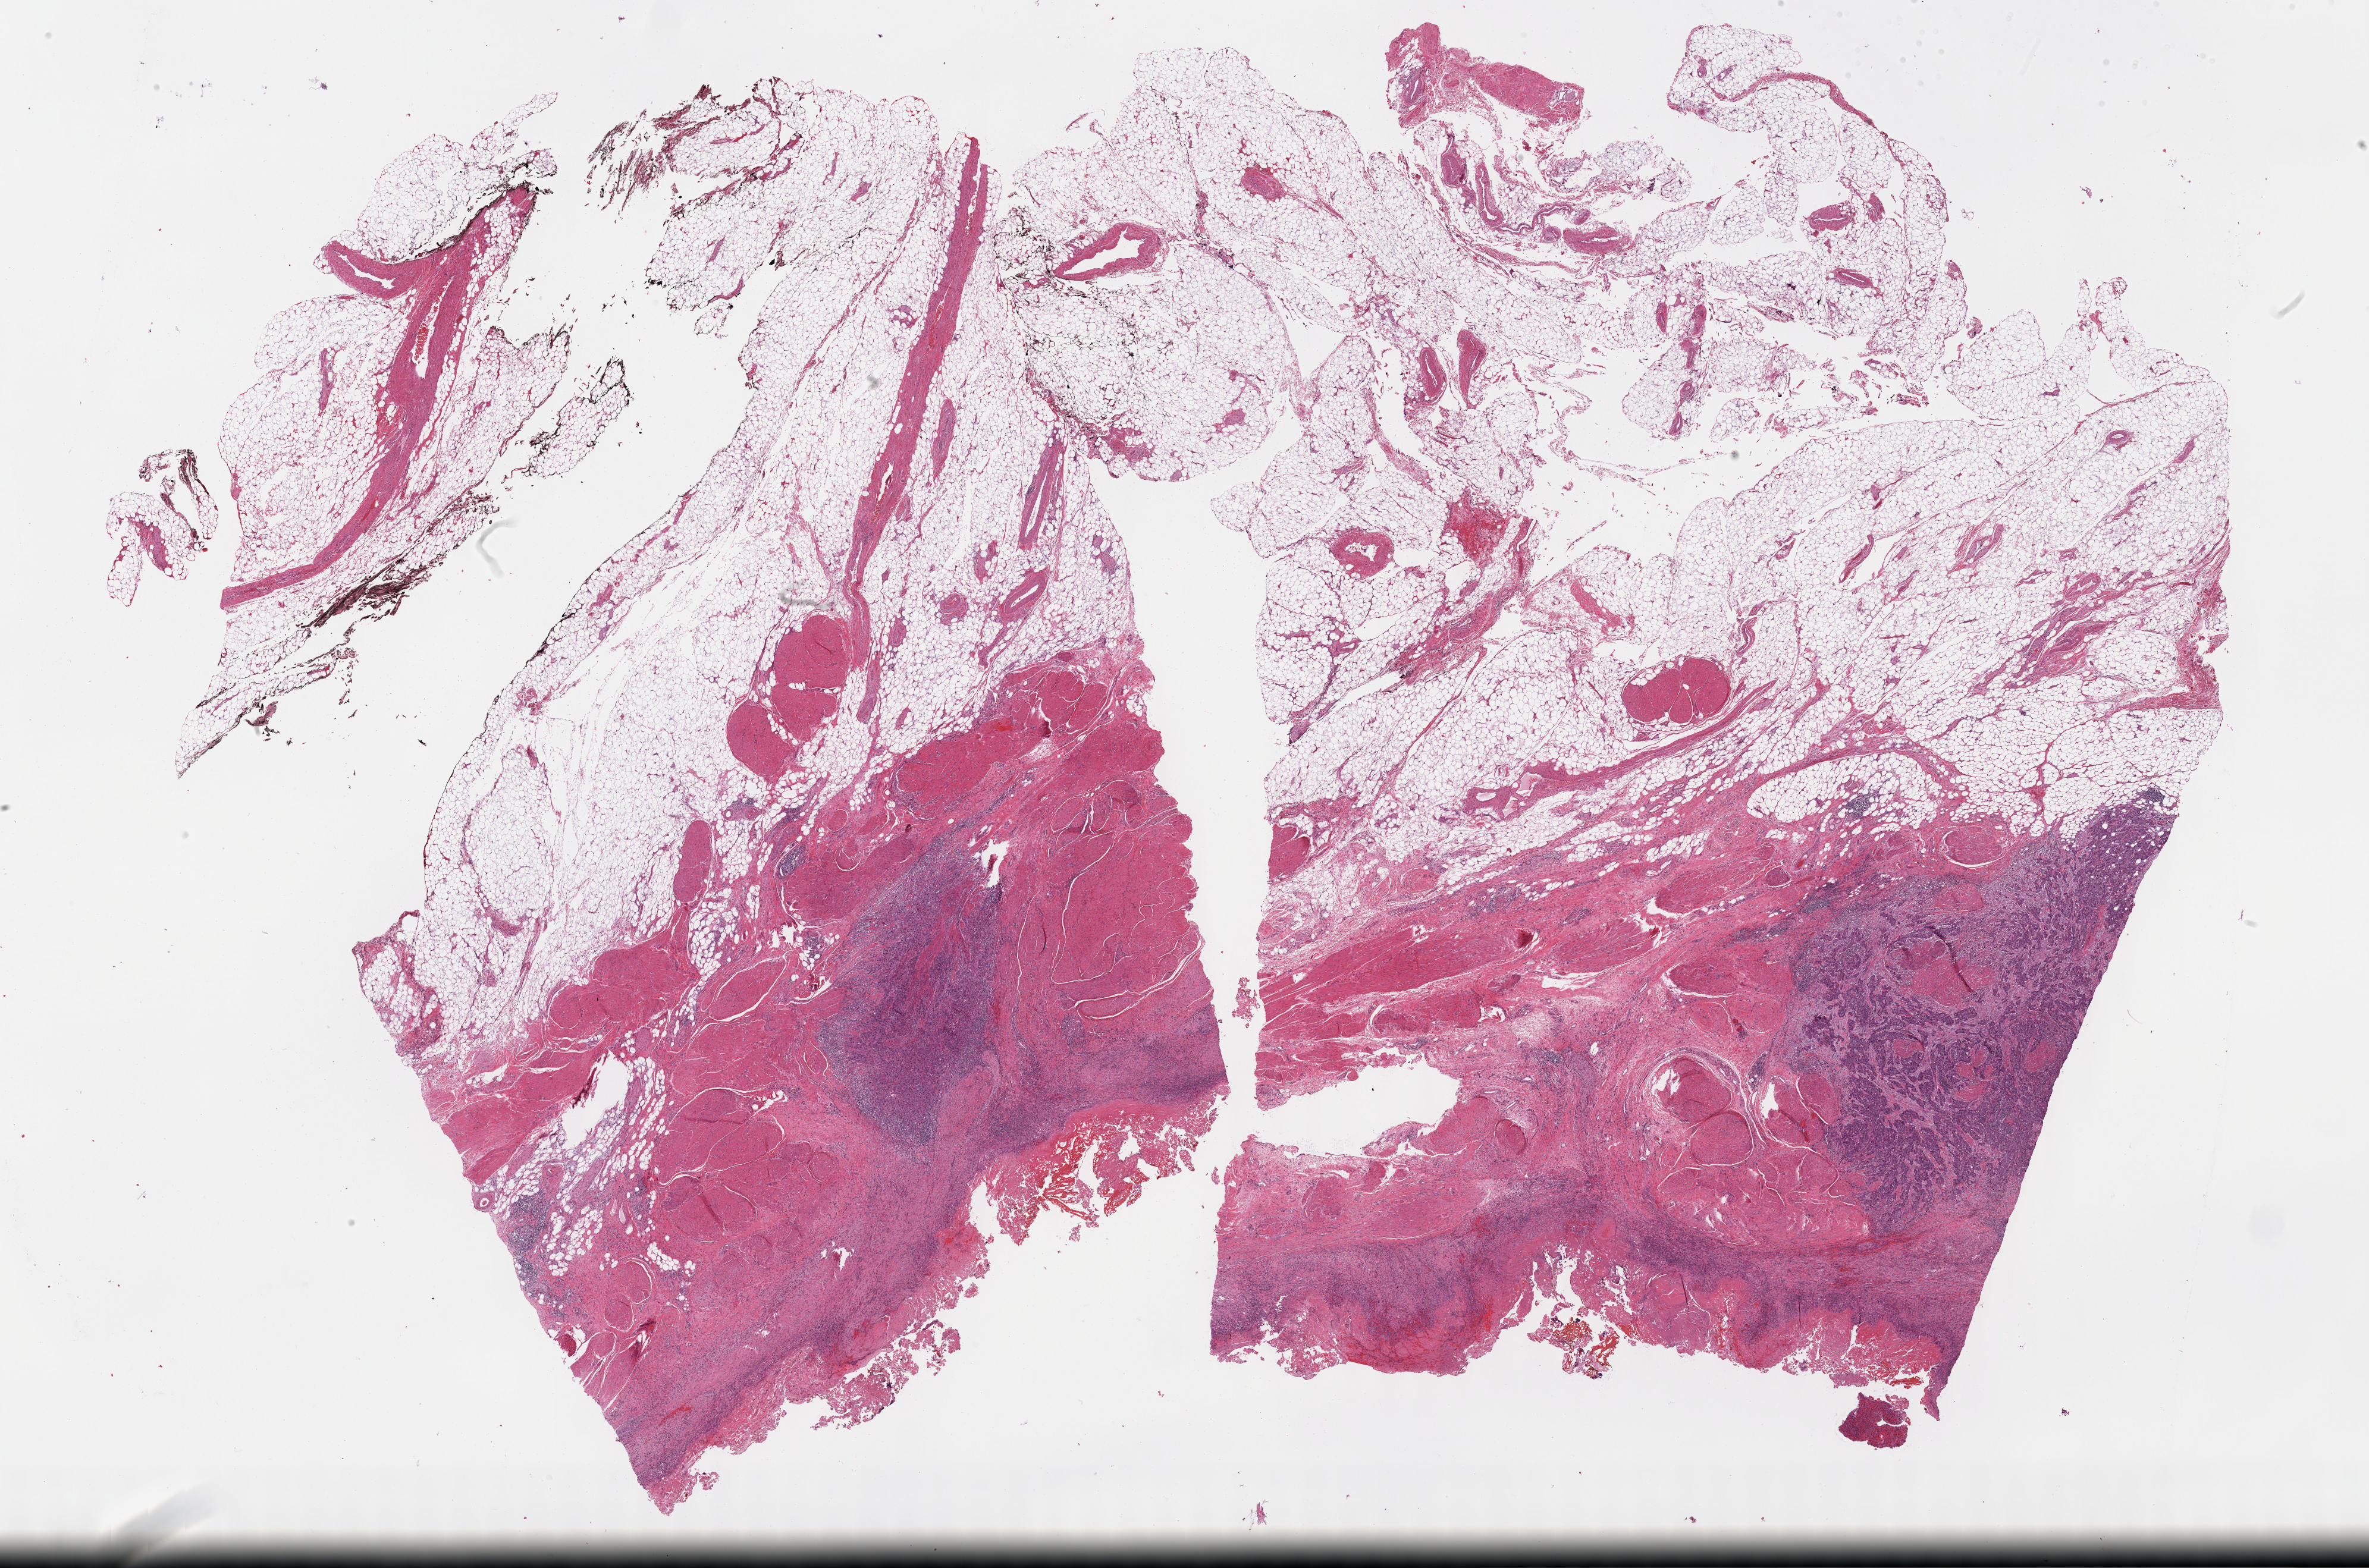
H&E whole-slide image — low-resolution overview of the scanned area, about 32.2 x 21.3 mm; FFPE section; bladder, primary tumour sample. Male patient; age at initial diagnosis 82 years. Histologic grade: high grade.
* AJCC pathologic stage: III (7th edition)
* histologic diagnosis: Transitional cell carcinoma (lateral wall of bladder)
* lymph nodes positive (case pathology): 0 of 26 examined